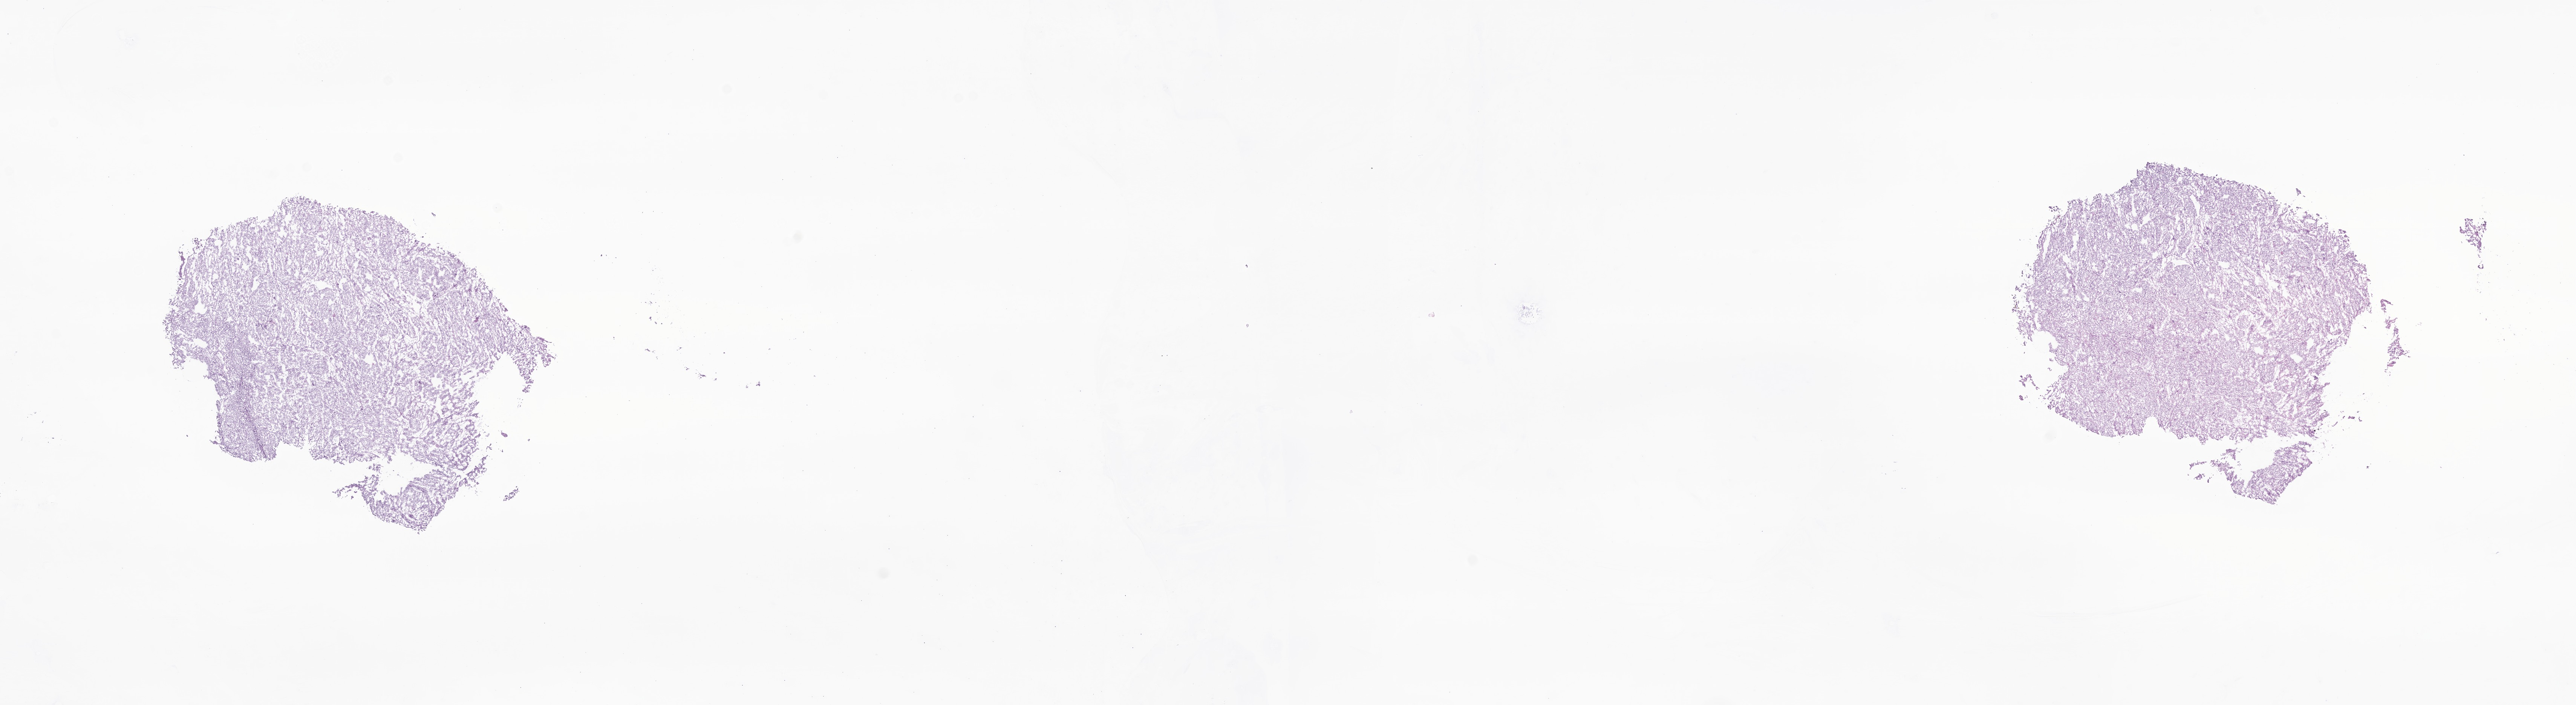
Haematoxylin and eosin whole-slide image of tumor tissue from the parietal lobe — low-resolution overview of the scanned area, about 28.8 x 7.9 mm; frozen section (OCT-embedded). Patient: female, age 182 months (15 years 2 months).
- diagnosis (ICD-O-3 morphology term): Glioma, malignant